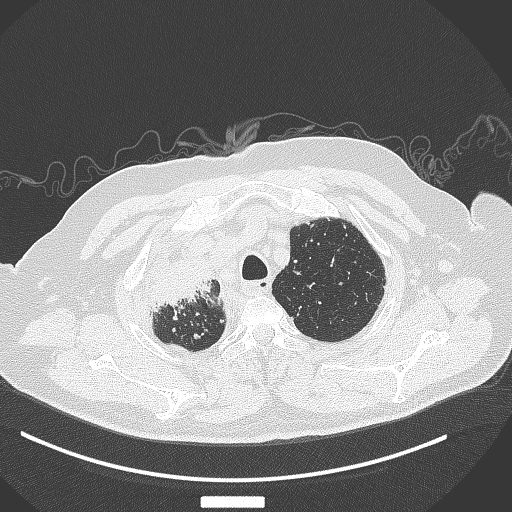
Chest CT, one axial slice. Slice 314 of 384 in the series (ordered by position). Reconstruction kernel B70f. 120 kVp. Lung window (W 1500 / L -600 HU). 1 mm slice thickness. 512 × 512 image matrix, field of view 400 × 400 mm. Patient: male, 69 years. Case-level facts recorded for this patient, not image findings: clinical TNM (as recorded): T4 N3 M1.
Outlined on this slice (bounding box drawn by a radiologist):
- lung tumour (recorded histology: adenocarcinoma): bounding box [x1, y1, x2, y2] px = [148, 264, 216, 317]